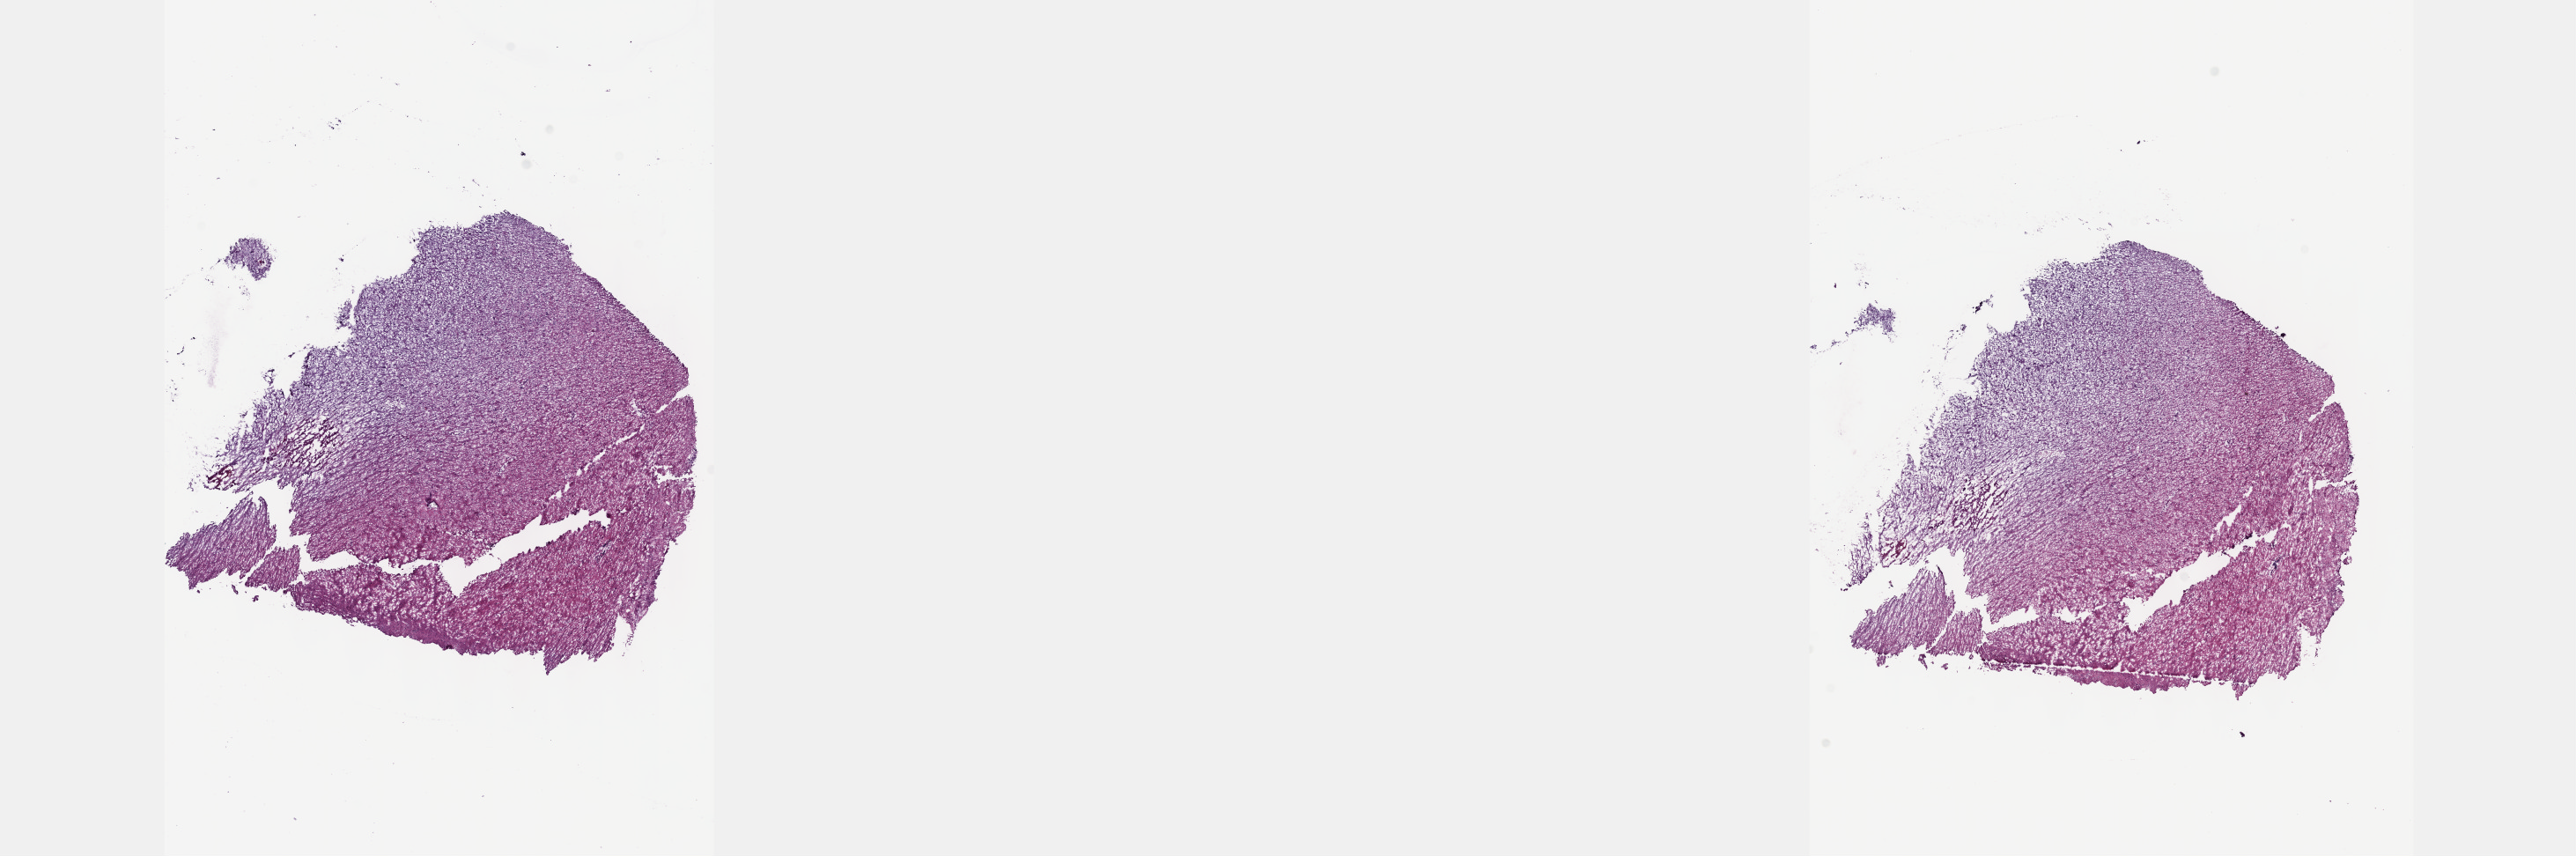
H&E whole-slide image, whole scanned area (about 23.6 x 7.9 mm, slide scanned at 40x) shown as a low-resolution overview, frozen section, brain, primary tumour sample. Male patient; age at initial diagnosis 63 years. Histologic grade: G3 (poorly differentiated). Slide review estimates, as recorded: tumour cells 25%, tumour nuclei 80%, normal cells 5%, stromal cells 70%, necrosis 0%. Infiltration values recorded for this section: lymphocyte infiltration 2%, monocyte infiltration 0%, neutrophil infiltration 0%.
Histologic diagnosis: Astrocytoma, anaplastic. Laterality: left.